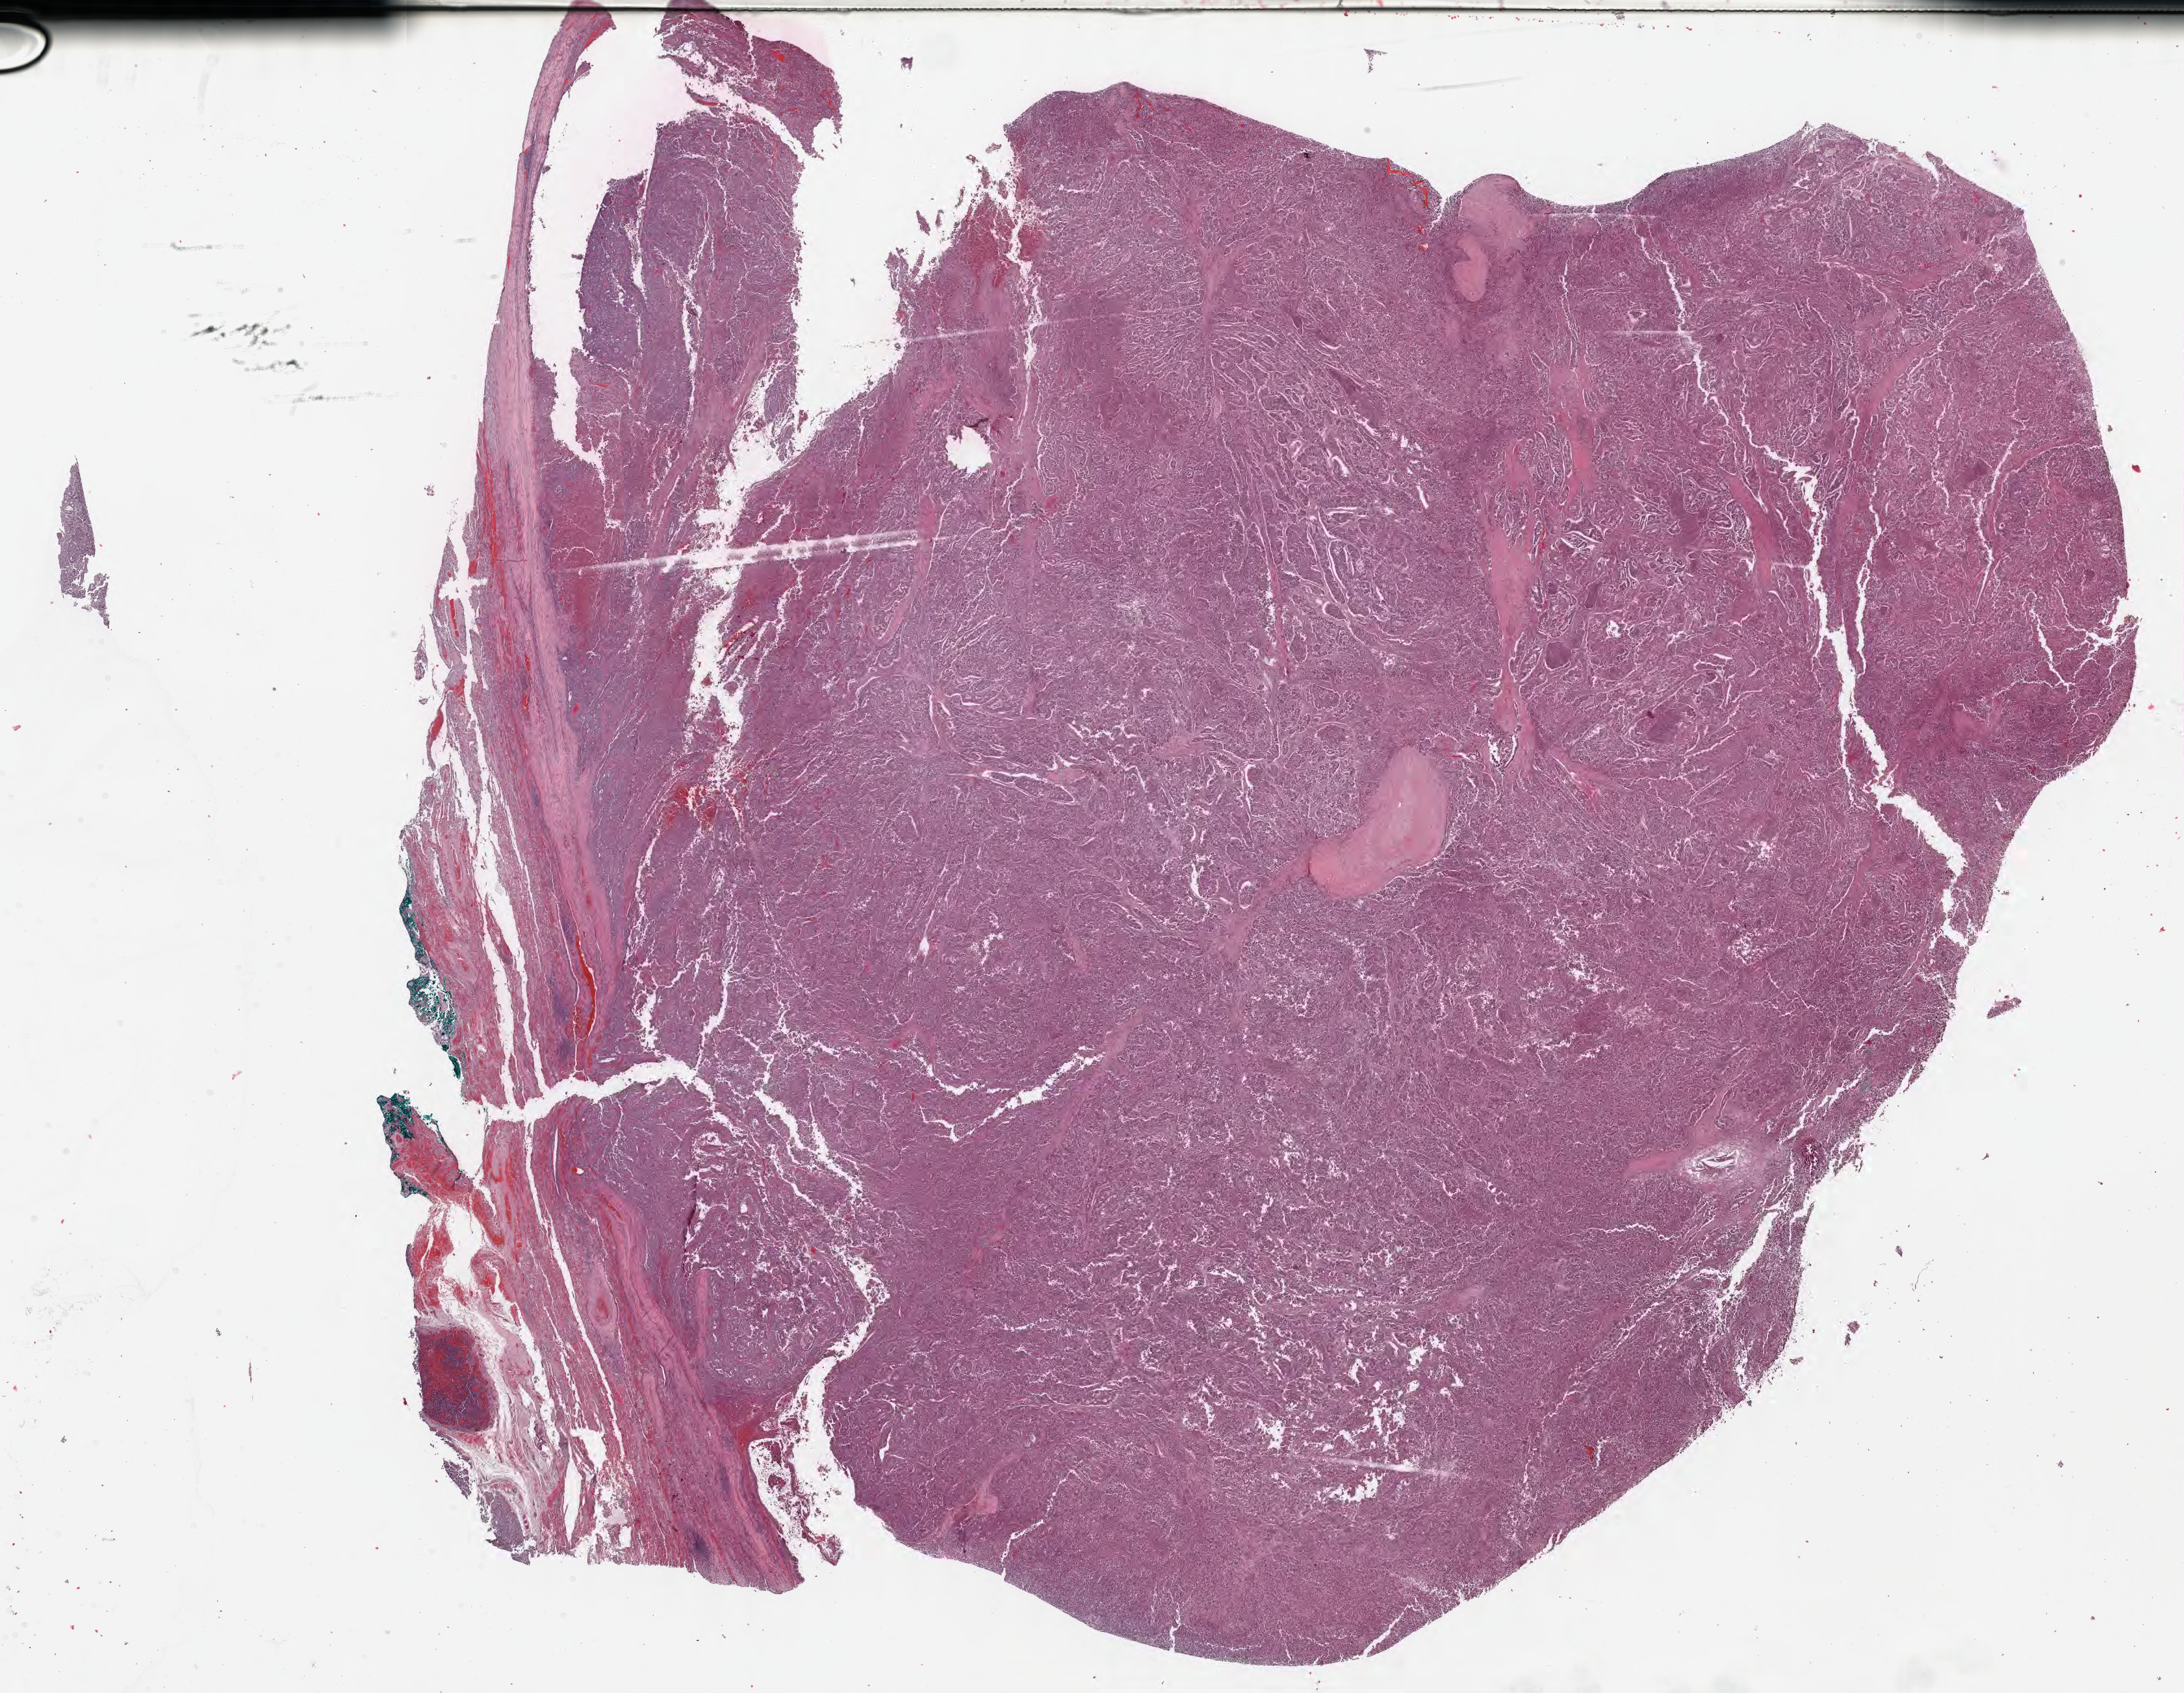
Hematoxylin and eosin (H&E) whole-slide image — shown as a low-resolution overview of the whole scanned area (about 27.2 x 21.1 mm). Tumor tissue. Site: lung (right). Patient male; age 52 years.
Diagnosis: Non-small cell carcinoma.